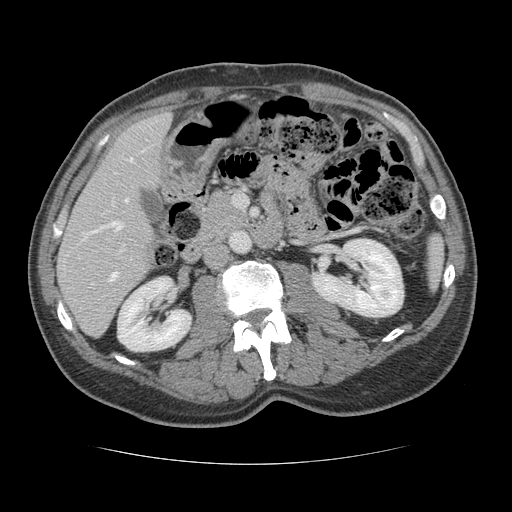
Contrast-enhanced abdominal CT, one axial slice; position 57 of 134 along the scan axis; intravenous contrast given; soft-tissue window (W 400 / L 40 HU); 2.5 mm slice thickness; 512 × 512 image matrix, field of view 377 × 377 mm. Male patient, age 68 years. From the clinical record (not read from this slice): diagnosis: colorectal cancer liver metastases, imaged before liver resection; multiple liver metastases: yes; largest metastasis: 2.2 cm; disease in both lobes: no.
Outlined on this slice (expert manual segmentation):
- hepatic veins: bounding box <89,150,144,234> (left, top, right, bottom; pixels)
- liver: <59,114,170,335>
- planned liver remnant (the part of the liver to remain after resection): <59,113,171,334>
- portal vein (with intrahepatic branches): <109,249,123,282>